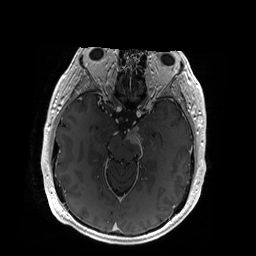
Brain MRI from a brain-tumour surgery series, one axial slice. Slice 117 of 192 in the series (ordered by position). T1-weighted post-contrast. 256 × 256 image matrix. From the clinical record (not read from this slice): histopathology: Glioblastoma; WHO grade: 4; IDH mutation: no.
Outlined on this slice (outlined manually by an expert reader):
- tumour: bounding box [x1, y1, x2, y2] px = [126, 127, 156, 153]